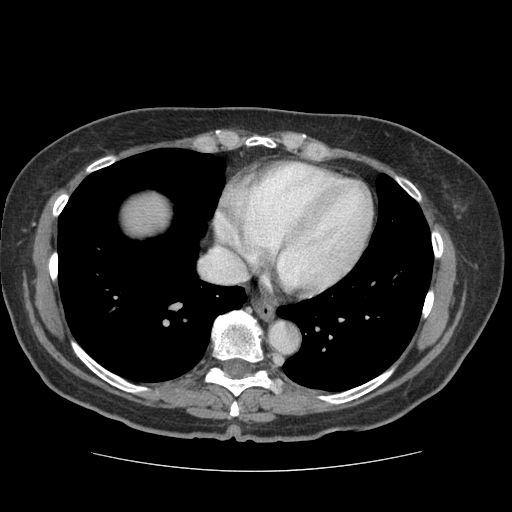
Contrast-enhanced abdominal CT (liver protocol), one axial slice; position 71 of 75 along the scan axis; 140 kVp; soft-tissue window (W 400 / L 40 HU); 2.5 mm slice thickness; 512 × 512 image matrix, field of view 360 × 360 mm. Case-level facts recorded for this patient, not image findings: diagnosis: hepatocellular carcinoma (patient treated with transarterial chemoembolisation; whether this scan precedes or follows treatment is not stated here); TNM stage (as recorded): Stage-I; Child-Pugh class: A; tumour differentiation: moderately differentiated; tumour nodularity: uninodular.
Outlined on this slice (semi-automatically segmented with operator editing):
- liver parenchyma outside the tumour (the mass and vessels are separate outlines, so this box may not span the whole liver): box from (x=122, y=192) to (x=168, y=236) px